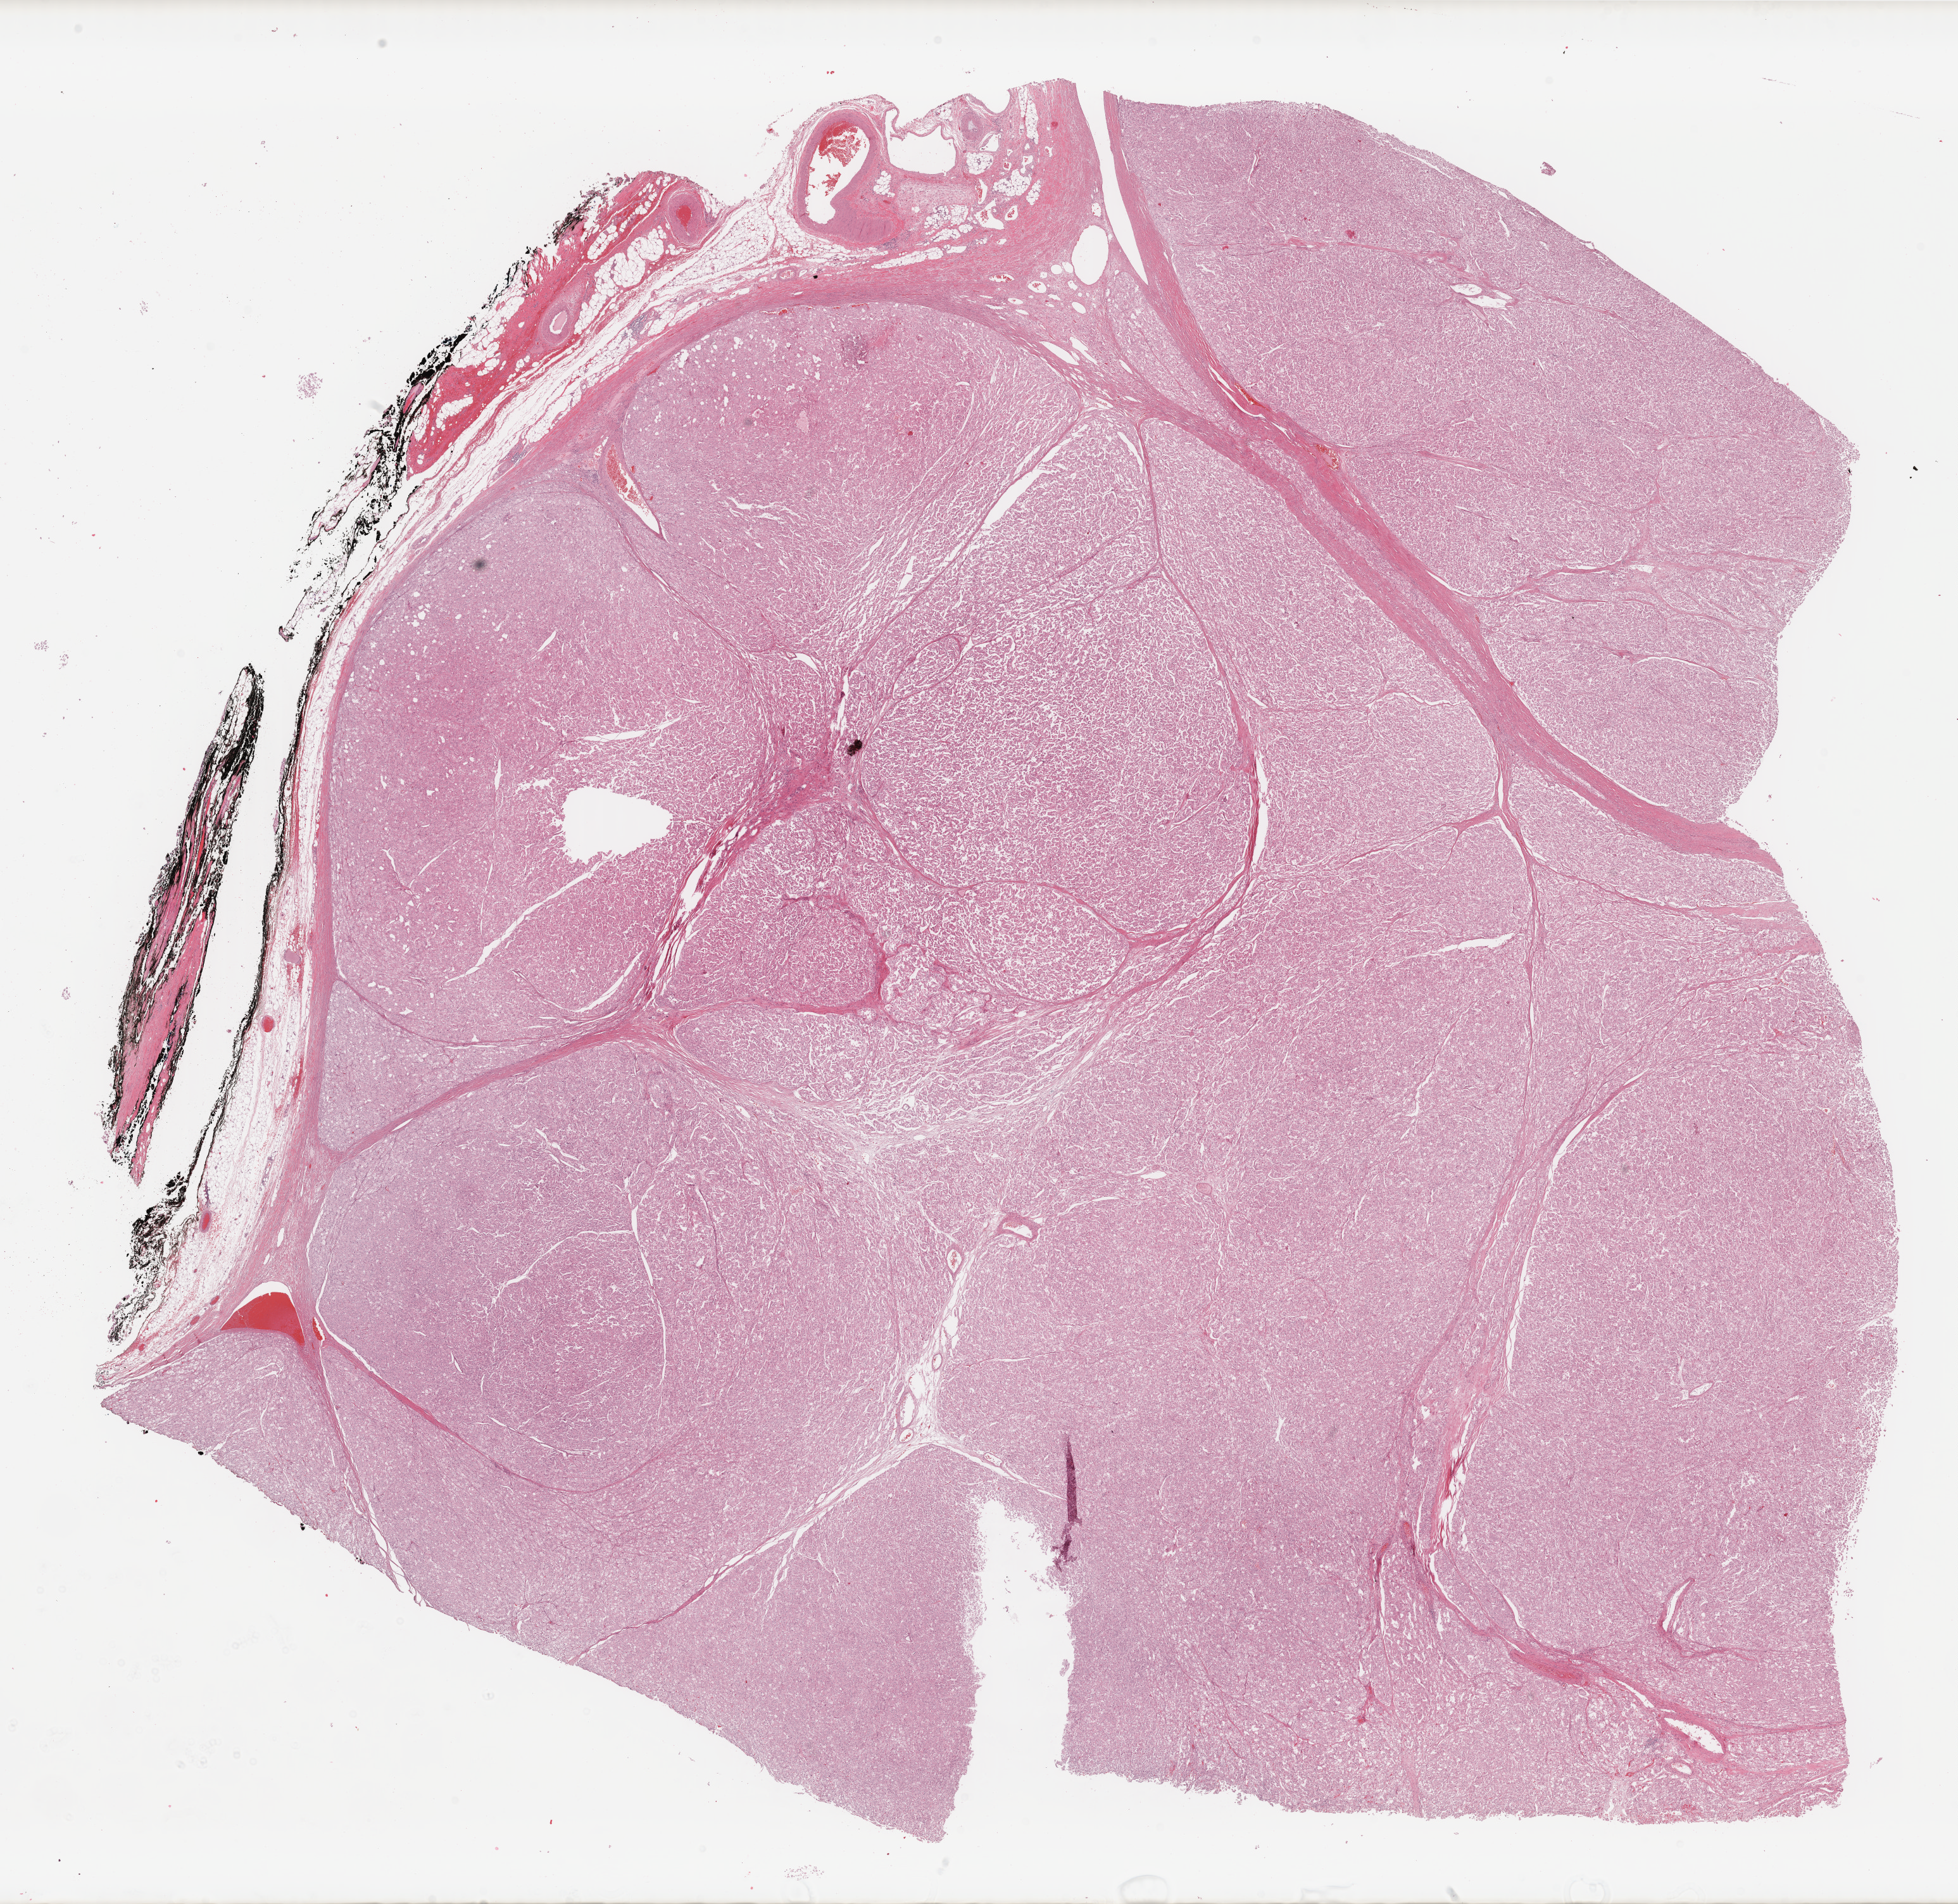
Digitized H&E-stained tissue section (whole slide) — whole scanned area (about 24.5 x 23.8 mm, acquisition: 40x scan) shown as a low-resolution overview; formalin-fixed paraffin-embedded (FFPE) diagnostic section; sample: primary tumour, kidney. Male, age 47 years at initial diagnosis. Composition of this section per pathologist review: tumour cells 80%, tumour nuclei 80%, normal cells 0%, stromal cells 20%, necrosis 0%. Infiltration values recorded for this section: lymphocyte infiltration 2%, monocyte infiltration 1%, neutrophil infiltration 1%.
- diagnosis: Renal cell carcinoma, chromophobe type
- AJCC pathologic stage: II